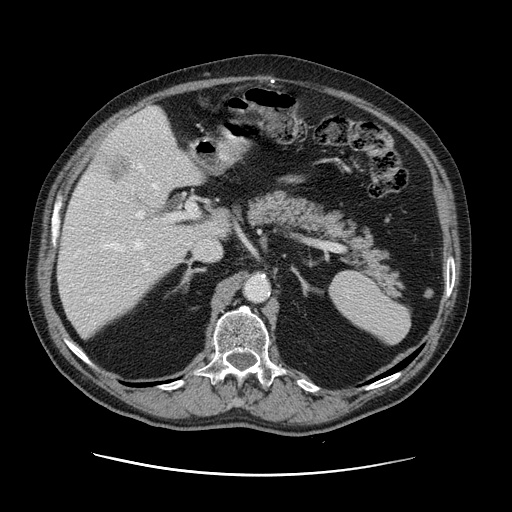
Contrast-enhanced abdominal CT, one axial slice. Position 75 of 141 along the scan axis. 120 kVp. Intravenous contrast given. Soft-tissue window (W 400 / L 40 HU). 2.5 mm slice thickness. 512 × 512 image matrix. Male patient, age 72 years. Case-level facts recorded for this patient, not image findings: diagnosis: colorectal cancer liver metastases, imaged before liver resection; multiple liver metastases: yes; largest metastasis: 5.4 cm.
Outlined on this slice (outlined manually by an expert reader):
- hepatic veins: bounding box [x1, y1, x2, y2] px = [105, 164, 158, 251]
- liver: [58, 107, 231, 337]
- planned liver remnant (the part of the liver to remain after resection): [58, 169, 231, 337]
- portal vein (with intrahepatic branches): [90, 201, 197, 301]
- liver metastasis: [106, 157, 130, 185]